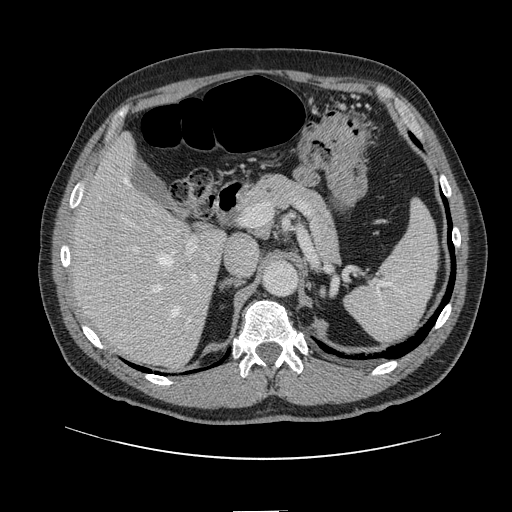
Contrast-enhanced abdominal CT, one axial slice. Position 82 of 161 along the scan axis. Intravenous contrast given. Soft-tissue window (W 400 / L 40 HU). 2.5 mm slice thickness. 512 × 512 image matrix, field of view 412 × 412 mm. Male patient, age 66 years. From the clinical record (not read from this slice): diagnosis: colorectal cancer liver metastases, imaged before liver resection; multiple liver metastases: no; largest metastasis: 3.5 cm.
Annotated regions visible in this slice (outlined manually by an expert reader):
- hepatic veins: bounding box (x1, y1, x2, y2) in pixels: (100, 177, 179, 317)
- liver: (75, 137, 223, 366)
- planned liver remnant (the part of the liver to remain after resection): (75, 137, 185, 300)
- portal vein (with intrahepatic branches): (120, 215, 199, 299)